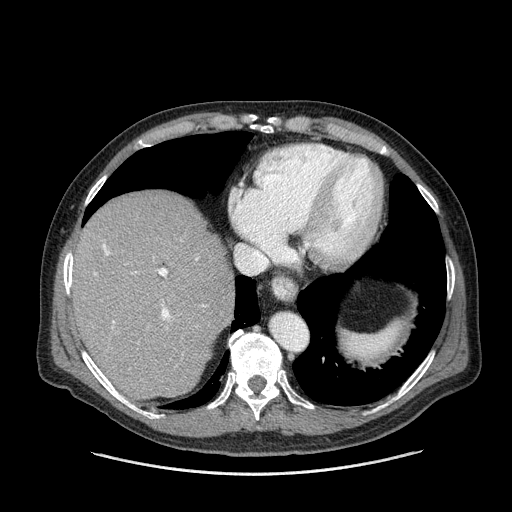
Contrast-enhanced abdominal CT (liver protocol), one axial slice. Slice 122 of 180 in the series (ordered by position). Reconstruction kernel STANDARD. One of 2 acquisitions stored at this slice position. Soft-tissue window (W 400 / L 40 HU). 512 × 512 image matrix, field of view 420 × 420 mm. Case-level facts recorded for this patient, not image findings: diagnosis: hepatocellular carcinoma (patient treated with transarterial chemoembolisation; whether this scan precedes or follows treatment is not stated here); TNM stage (as recorded): Stage-II; Child-Pugh class: A; tumour nodularity: multinodular; tumour size: 2.8 cm.
Annotated regions visible in this slice (semi-automatically segmented with operator editing):
- abdominal aorta: bounding box (x1, y1, x2, y2) in pixels: (271, 314, 307, 350)
- liver parenchyma outside the tumour (the mass and vessels are separate outlines, so this box may not span the whole liver): (74, 192, 234, 398)
- liver vessels: (94, 244, 205, 328)